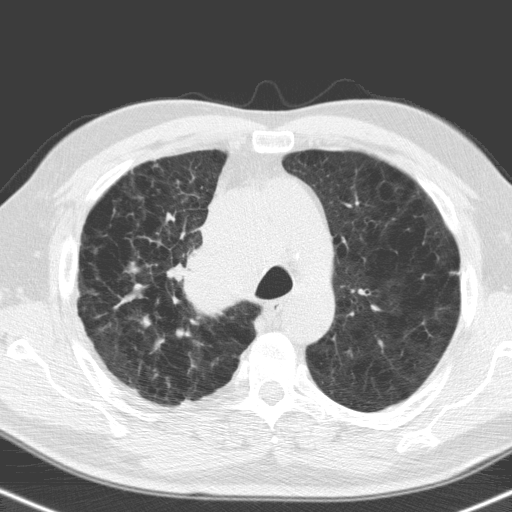
Low-dose screening chest CT, one axial slice. Position 122 of 160 along the scan axis. 120 kVp. Lung window (W 1500 / L -600 HU). 512 × 512 image matrix.
Annotated regions visible in this slice (manually delineated by an expert):
- lesion 1 (tumor, hilum of right lung): bounding box [x1, y1, x2, y2] px = [172, 246, 248, 312]